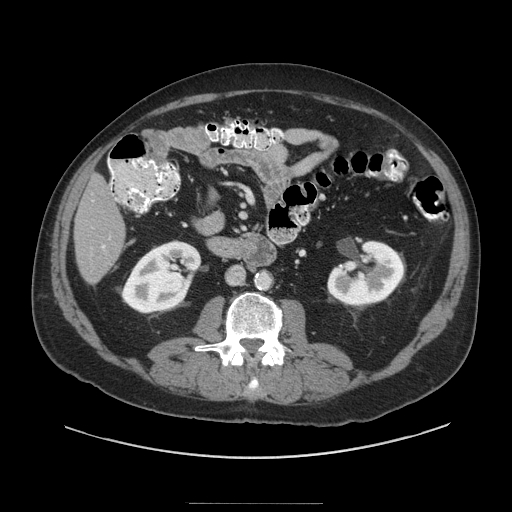
Contrast-enhanced abdominal CT (liver protocol), one axial slice. Slice 25 of 91 in the series (ordered by position). Reconstruction kernel STANDARD. Soft-tissue window (W 400 / L 40 HU). 2.5 mm slice thickness. 512 × 512 image matrix, field of view 440 × 440 mm. From the clinical record (not read from this slice): diagnosis: hepatocellular carcinoma (patient treated with transarterial chemoembolisation; whether this scan precedes or follows treatment is not stated here); TNM stage (as recorded): Stage-I; Child-Pugh class: A; tumour differentiation: well differentiated; tumour nodularity: uninodular.
Annotated regions visible in this slice (semi-automatic segmentation, software-assisted and operator-edited):
- liver parenchyma outside the tumour (the mass and vessels are separate outlines, so this box may not span the whole liver): bounding box (x1, y1, x2, y2) in pixels: (74, 174, 124, 284)
- liver vessels: (102, 238, 110, 249)